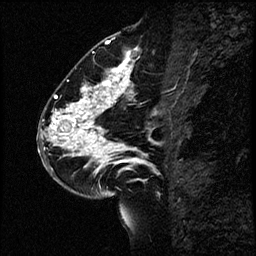
Breast MRI (dynamic contrast-enhanced), one sagittal slice; slice 33 of 60 in the series (ordered by position); dynamic contrast-enhanced study with each time point stored as its own series, time point 2 of 4 at this slice position (early post-contrast, ordered by acquisition time); 1.5 T; TE 4.2 ms, TR 17.6 ms; 2 mm slice thickness; 256 × 256 image matrix. Patient: female, 43 years. From the clinical record (not read from this slice): setting: breast cancer imaged before/during neoadjuvant chemotherapy.
Structures marked on this image (semi-automatic segmentation, software-assisted and operator-edited):
- analysis volume of interest (the breast-tissue region the enhancement analysis was run in; not a lesion): bounding box (x1, y1, x2, y2) in pixels: (40, 56, 164, 191)
- tumour enhancement mask (voxels above the 100 % enhancement threshold inside the analysis volume of interest): (41, 58, 155, 166)